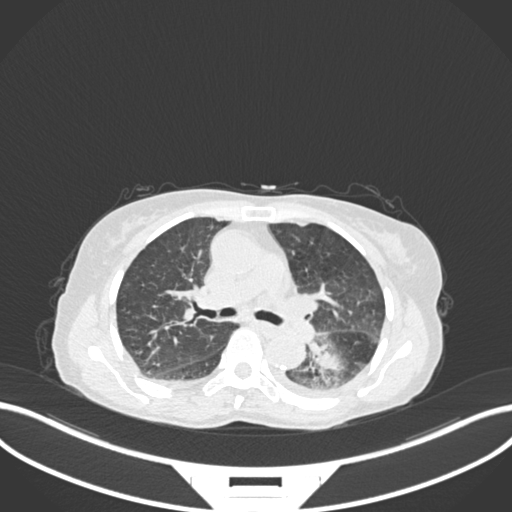
Chest CT, one axial slice. Slice 108 of 233 in the series (ordered by position). 120 kVp. Lung window (W 1500 / L -600 HU). 512 × 512 image matrix. Patient: female, 78 years. From the clinical record (not read from this slice): clinical TNM (as recorded): T3 N0 M1.
Annotated regions visible in this slice (bounding box drawn by a radiologist):
- lung tumour (recorded histology: squamous cell carcinoma): bounding box [x1, y1, x2, y2] px = [301, 328, 355, 389]